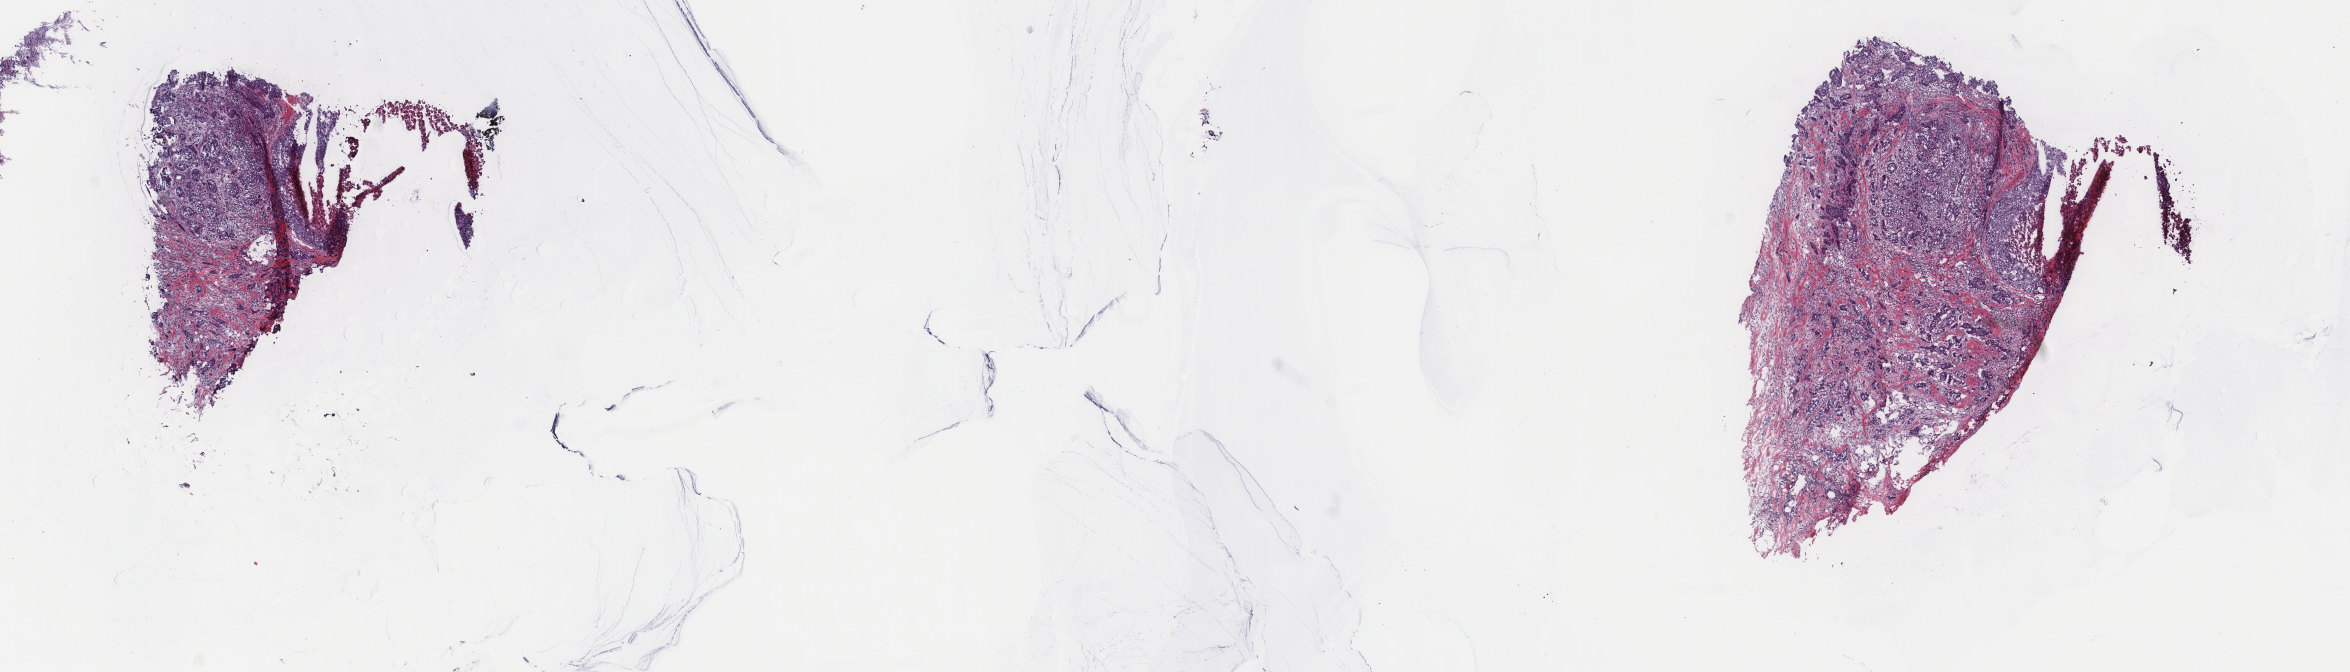
Whole-slide histology image, H&E — whole scanned area (about 18.7 x 5.3 mm, acquisition: 40x scan) shown as a low-resolution overview; frozen section from the top of the tissue portion; breast, primary tumour sample. Female patient; age at initial diagnosis 49 years. Composition of this section per pathologist review: tumour cells 60%, tumour nuclei 70%, normal cells 0%, stromal cells 35%, necrosis 5%. Infiltration values recorded for this section: lymphocyte infiltration 0%, monocyte infiltration 0%, neutrophil infiltration 0%.
AJCC pathologic stage: IIB (7th edition). TNM: T2 N1a M0. Lymph nodes positive (case pathology): 3 of 16 examined. Diagnosis: Infiltrating duct carcinoma, NOS.